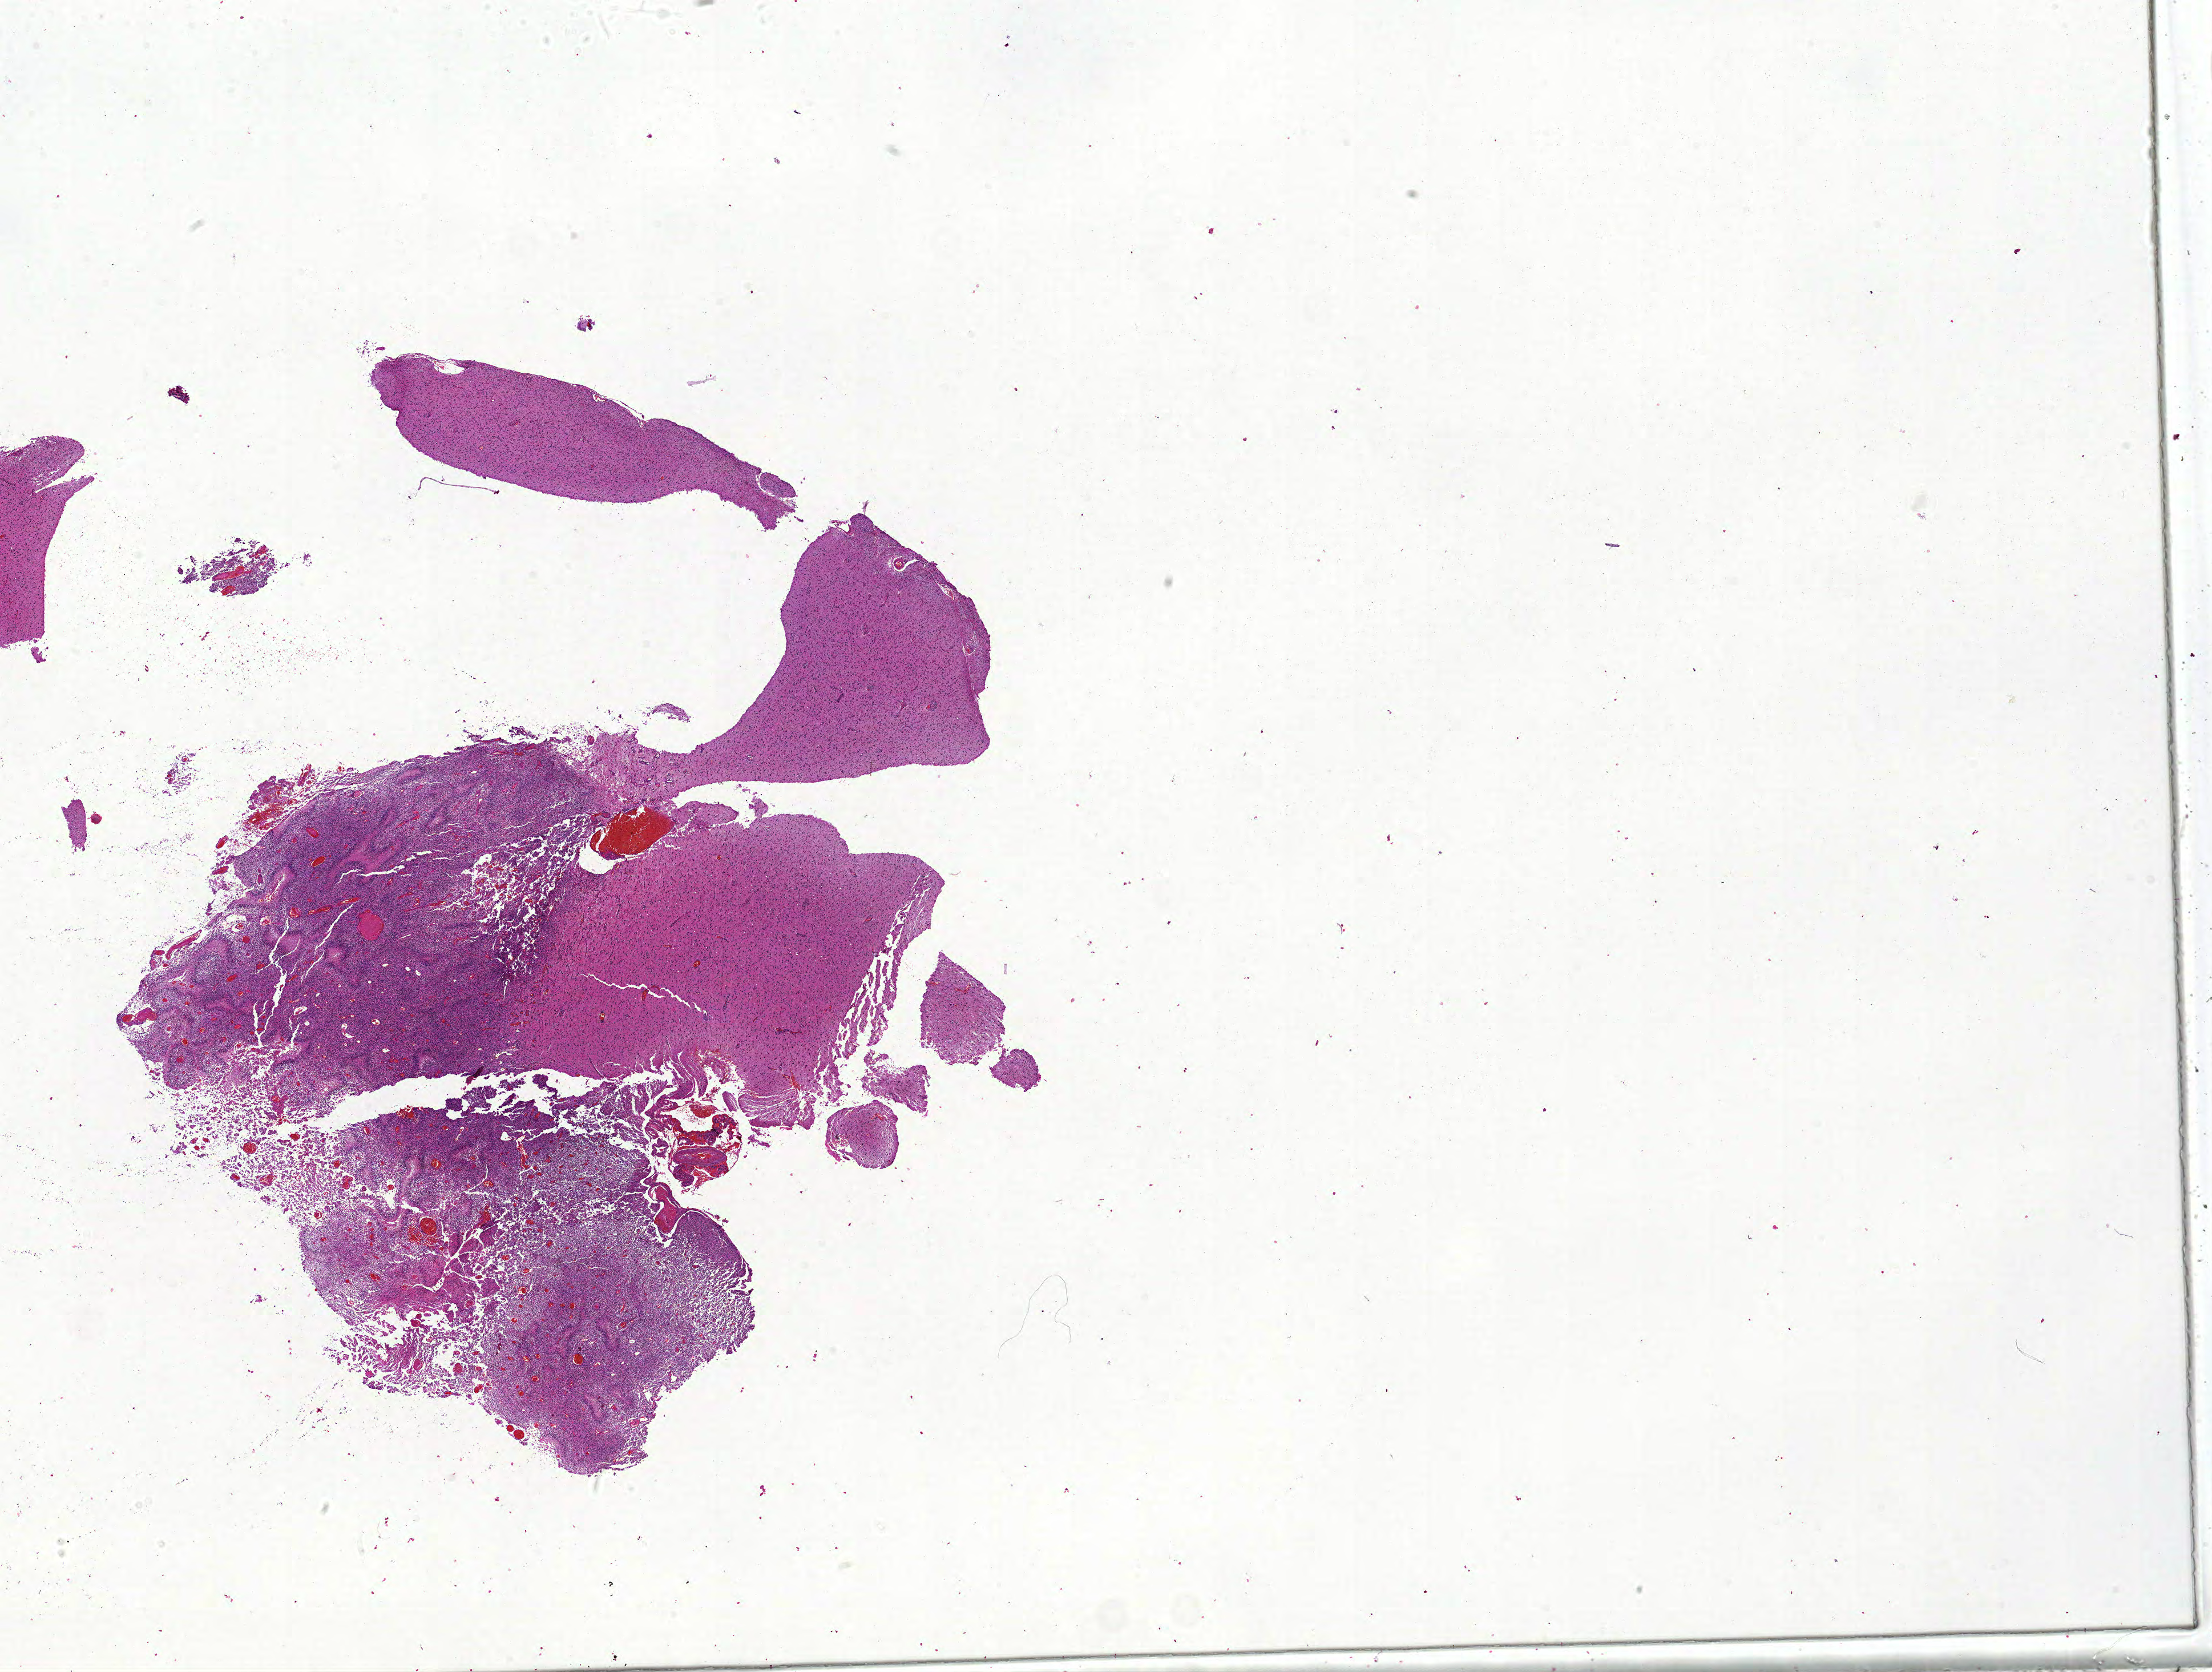
Digitized H&E tissue section (whole slide) — shown as a low-resolution overview of the whole scanned area (about 31.0 x 23.4 mm); formalin-fixed paraffin-embedded (FFPE) diagnostic section; brain, primary tumour sample. Female, age 49 years at initial diagnosis.
Diagnosis: Glioblastoma.